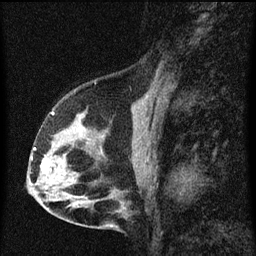
Breast MRI (dynamic contrast-enhanced), one sagittal slice. Position 35 of 60 along the scan axis. Dynamic contrast-enhanced series, image 2 of 3 at this slice position (ordered by acquisition). 1.5 T. TE 4.2 ms, TR 8 ms. 256 × 256 image matrix, field of view 180 × 180 mm. Female patient, age 56 years.
Outlined on this slice (semi-automatically segmented with operator editing):
- analysis volume of interest (the breast-tissue region the enhancement analysis was run in; not a lesion): bounding box <34,114,102,181> (left, top, right, bottom; pixels)
- tumour enhancement mask (voxels above the 70 % enhancement threshold inside the analysis volume of interest): <34,148,48,172>